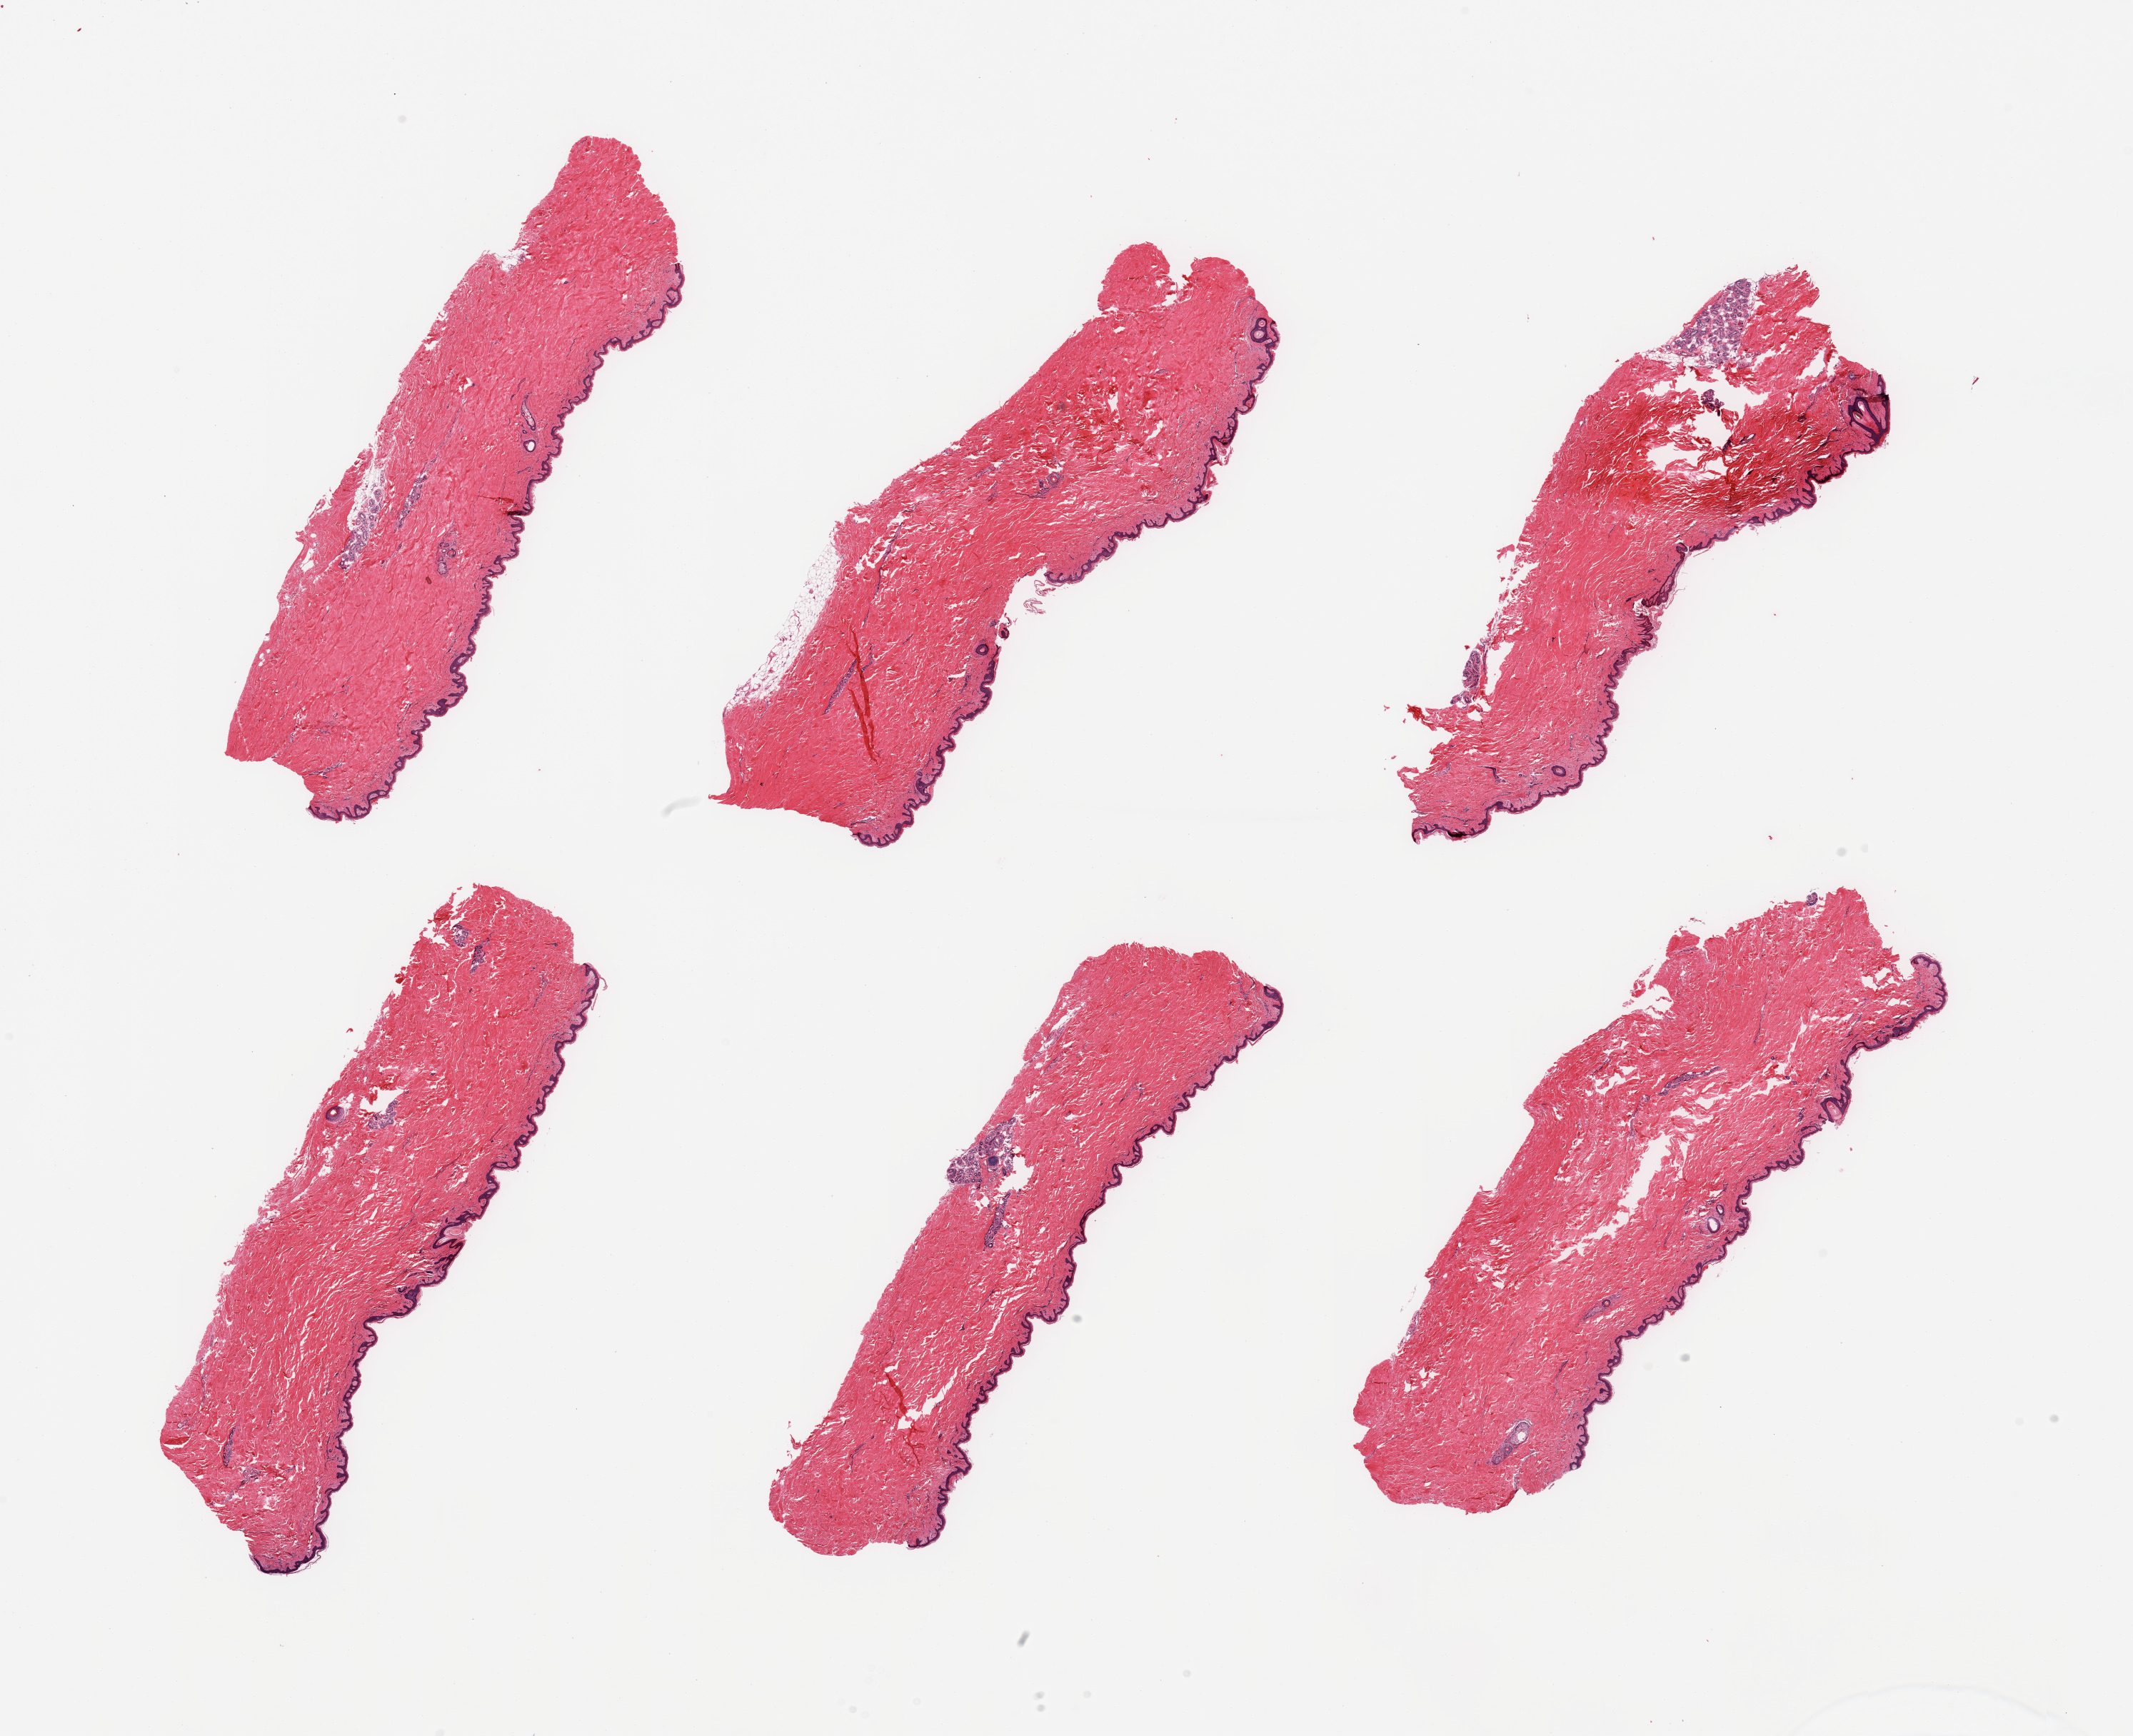
Whole-slide image, H&E stain — low-resolution overview of the scanned area, about 23.6 x 19.2 mm; PAXgene-fixed, paraffin-embedded tissue; sampled site (target tissue): skin of suprapubic region; donor tissue sample. Donor sex: male.
• review note (as recorded): 6 pieces; essentially well trimmed with small amounts of dermal fat